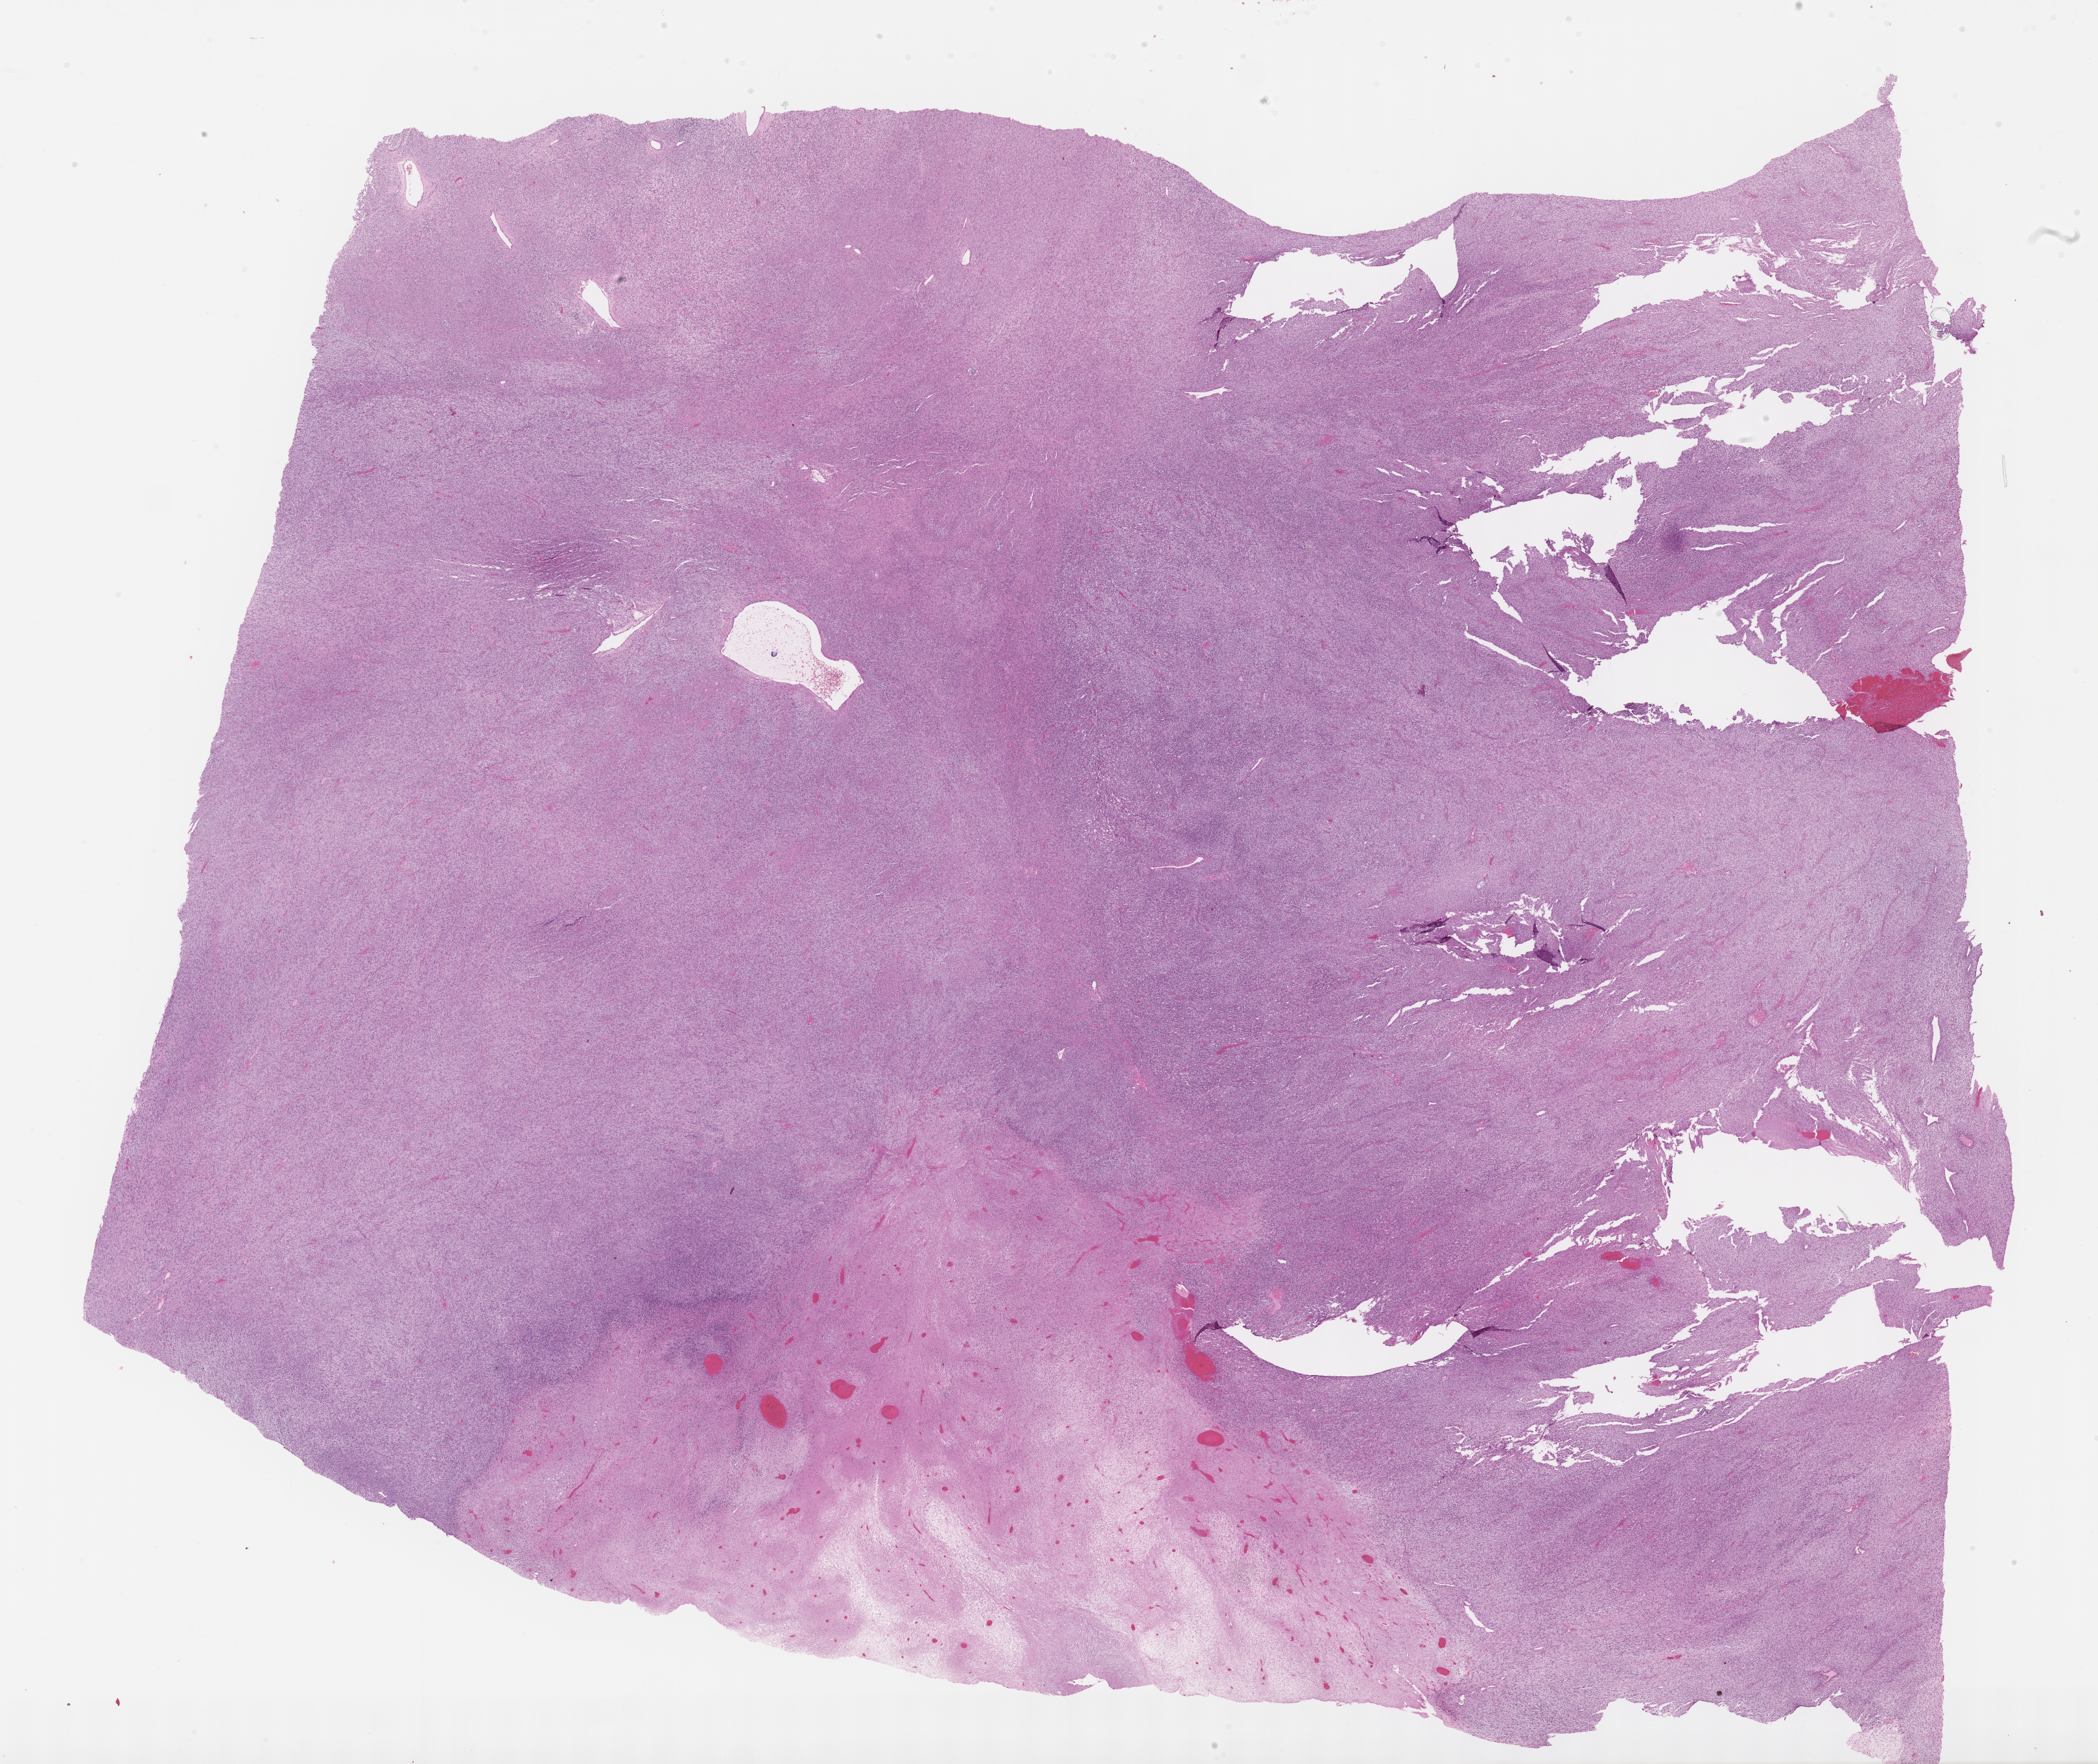
Digitized hematoxylin and eosin (H&E)-stained section of tumor tissue, shown as a low-resolution overview of the whole scanned area (about 26.2 x 22.0 mm), FFPE section, sample anatomic site: scrotum, left. Male patient, age at diagnosis 14.5 years.
Primary site (case record): testis-paratesticular. Metastatic status at presentation (as recorded): non-metastatic (confirmed). Diagnosis: rhabdomyosarcoma; histological classification: spindle cell rhabdomyosarcoma. Stage (as recorded): 1.